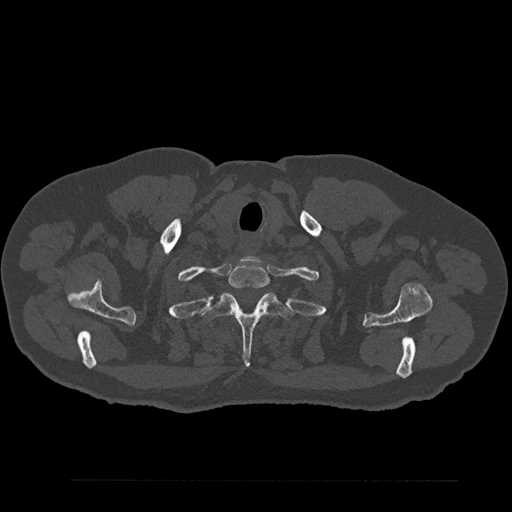
CT including the spine, one axial slice. Position 732 of 797 along the scan axis. Reconstruction kernel Br40s/3. Bone window (W 1800 / L 400 HU). 0.5 mm slice thickness. 512 × 512 image matrix. Male patient, age 61 years. From the clinical record (not read from this slice): primary cancer: prostate.
Structures marked on this image (semi-automatically segmented with operator editing):
- T1 vertebra: bounding box [x1, y1, x2, y2] px = [228, 263, 269, 289]
- T2 vertebra: [202, 293, 292, 365]